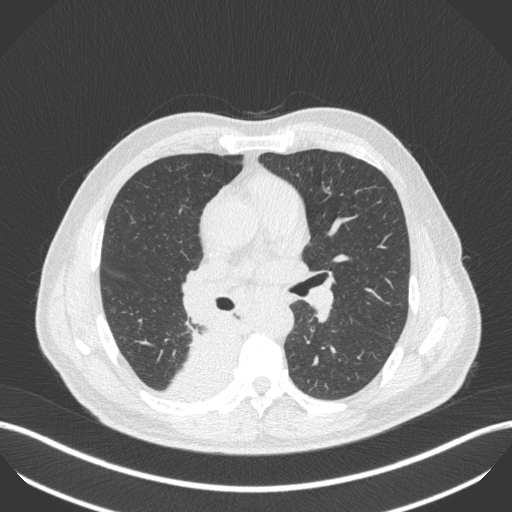
Chest CT, one axial slice. Position 262 of 451 along the scan axis. Reconstruction kernel B31f. 100 kVp. Lung window (W 1500 / L -600 HU). 1 mm slice thickness. 512 × 512 image matrix, field of view 400 × 400 mm. Patient: male, 61 years. From the clinical record (not read from this slice): clinical TNM (as recorded): T1 N0 M0.
Structures marked on this image (rectangle marked by the reading radiologist):
- lung tumour (recorded histology: small cell carcinoma): bounding box <154,323,243,403> (left, top, right, bottom; pixels)